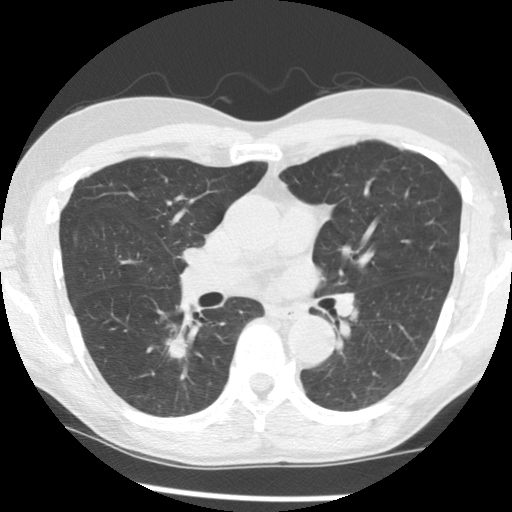
Low-dose screening chest CT, one axial slice; slice 78 of 145 in the series (ordered by position); reconstruction kernel STANDARD; 140 kVp; lung window (W 1500 / L -600 HU); 512 × 512 image matrix.
Outlined on this slice (expert manual segmentation):
- lesion 1 (tumor, lower lobe of right lung): box from (x=166, y=332) to (x=187, y=359) px